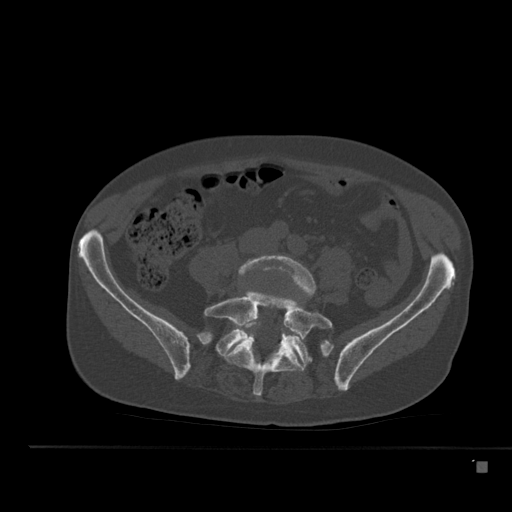
CT including the spine, one axial slice. Position 127 of 517 along the scan axis. Reconstruction kernel Br40s. 120 kVp. Bone window (W 1800 / L 400 HU). 1.5 mm slice thickness. 512 × 512 image matrix, field of view 408 × 408 mm. Male patient, age 70 years. From the clinical record (not read from this slice): primary cancer: renal.
Annotated regions visible in this slice (semi-automatically segmented with operator editing):
- L4 vertebra: bounding box [x1, y1, x2, y2] px = [238, 255, 316, 334]
- L5 vertebra: [204, 292, 333, 396]